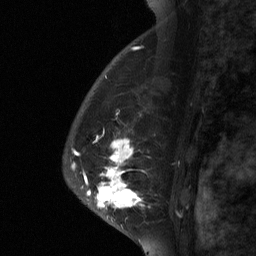
Breast MRI (dynamic contrast-enhanced), one sagittal slice; dynamic contrast-enhanced study with each time point stored as its own series, time point 2 of 3 at this slice position (early post-contrast, ordered by acquisition time); 1.5 T; TE 4.8 ms, TR 27 ms; 2 mm slice thickness; 256 × 256 image matrix. Female patient, age 56 years. From the clinical record (not read from this slice): setting: breast cancer imaged before/during neoadjuvant chemotherapy; receptor status: HER2-positive.
Outlined on this slice (semi-automatically segmented with operator editing):
- analysis volume of interest (the breast-tissue region the enhancement analysis was run in; not a lesion): bounding box (x1, y1, x2, y2) in pixels: (84, 104, 182, 229)
- tumour enhancement mask (voxels above the 90 % enhancement threshold inside the analysis volume of interest): (86, 138, 150, 209)